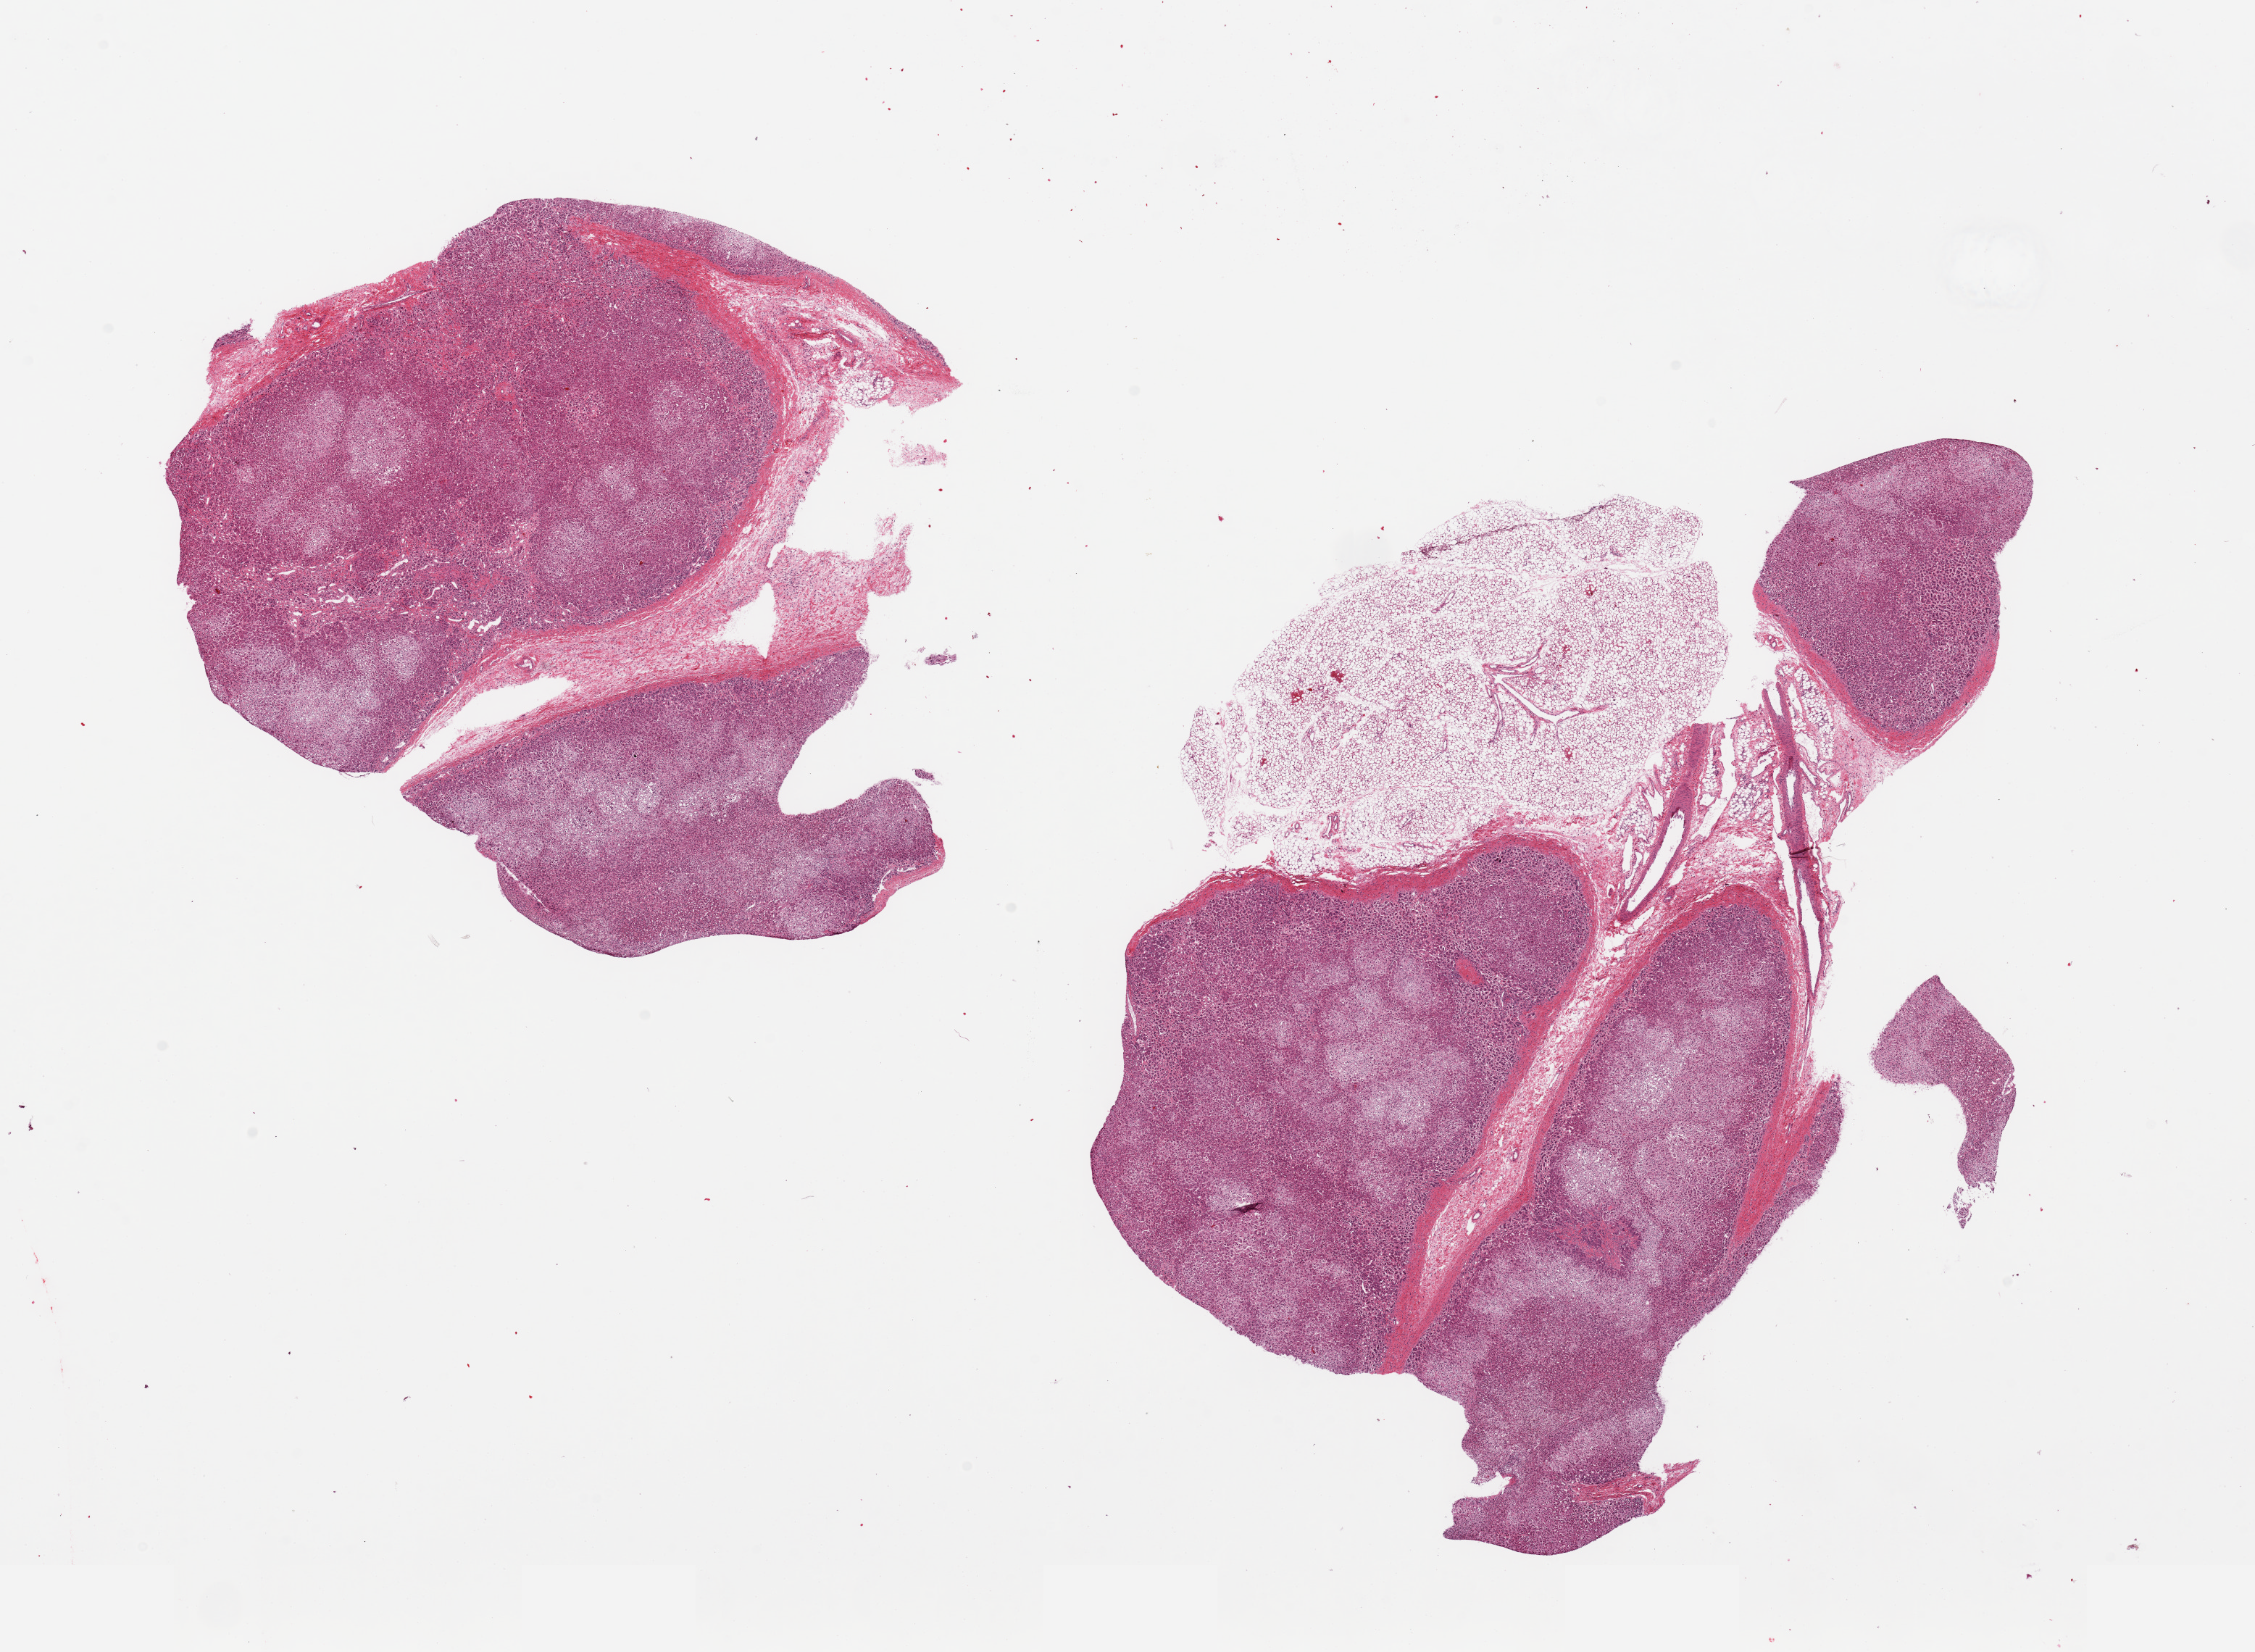
Whole-slide image, H&E stain — a low-resolution overview of the entire scanned area, about 24.6 x 18.0 mm. PAXgene-fixed, paraffin-embedded tissue. Target tissue: adrenal gland. Tissue donor sample. Donor sex: female.
• reviewer comment on this tissue sample: 2 pieces, one with 40% external fat